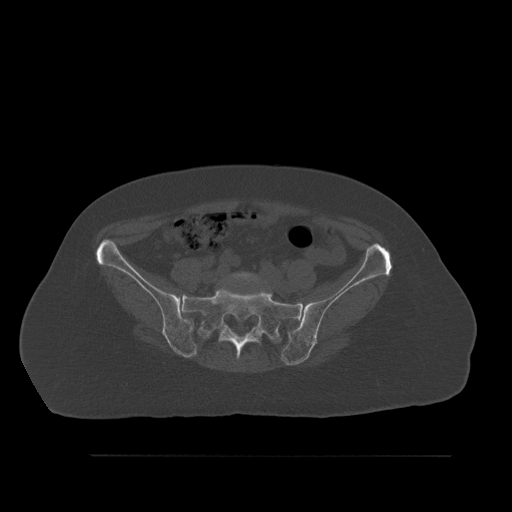
CT including the spine, one axial slice; slice 173 of 527 in the series (ordered by position); bone window (W 1800 / L 400 HU); 512 × 512 image matrix, field of view 470 × 470 mm. Patient: female, 73 years. Case-level facts recorded for this patient, not image findings: primary cancer: breast; vertebrae with lytic lesions (as recorded): L2.
Outlined on this slice (semi-automatic segmentation, software-assisted and operator-edited):
- L5 vertebra: bounding box [x1, y1, x2, y2] px = [229, 272, 261, 282]